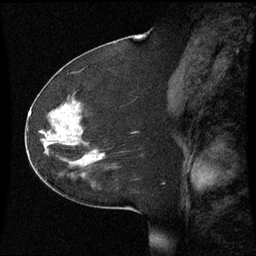
Breast MRI (dynamic contrast-enhanced), one sagittal slice. Slice 30 of 60 in the series (ordered by position). Dynamic contrast-enhanced series, image 2 of 3 at this slice position (ordered by acquisition). 1.5 T. TE 4.2 ms, TR 8.9 ms. 256 × 256 image matrix, field of view 220 × 220 mm. Patient: female, 51 years. From the clinical record (not read from this slice): setting: breast cancer imaged before/during neoadjuvant chemotherapy; receptor status: HR-positive, HER2-negative.
Outlined on this slice (semi-automatically segmented with operator editing):
- analysis volume of interest (the breast-tissue region the enhancement analysis was run in; not a lesion): bounding box <44,102,107,167> (left, top, right, bottom; pixels)
- tumour enhancement mask (voxels above the 70 % enhancement threshold inside the analysis volume of interest): <84,156,101,159>